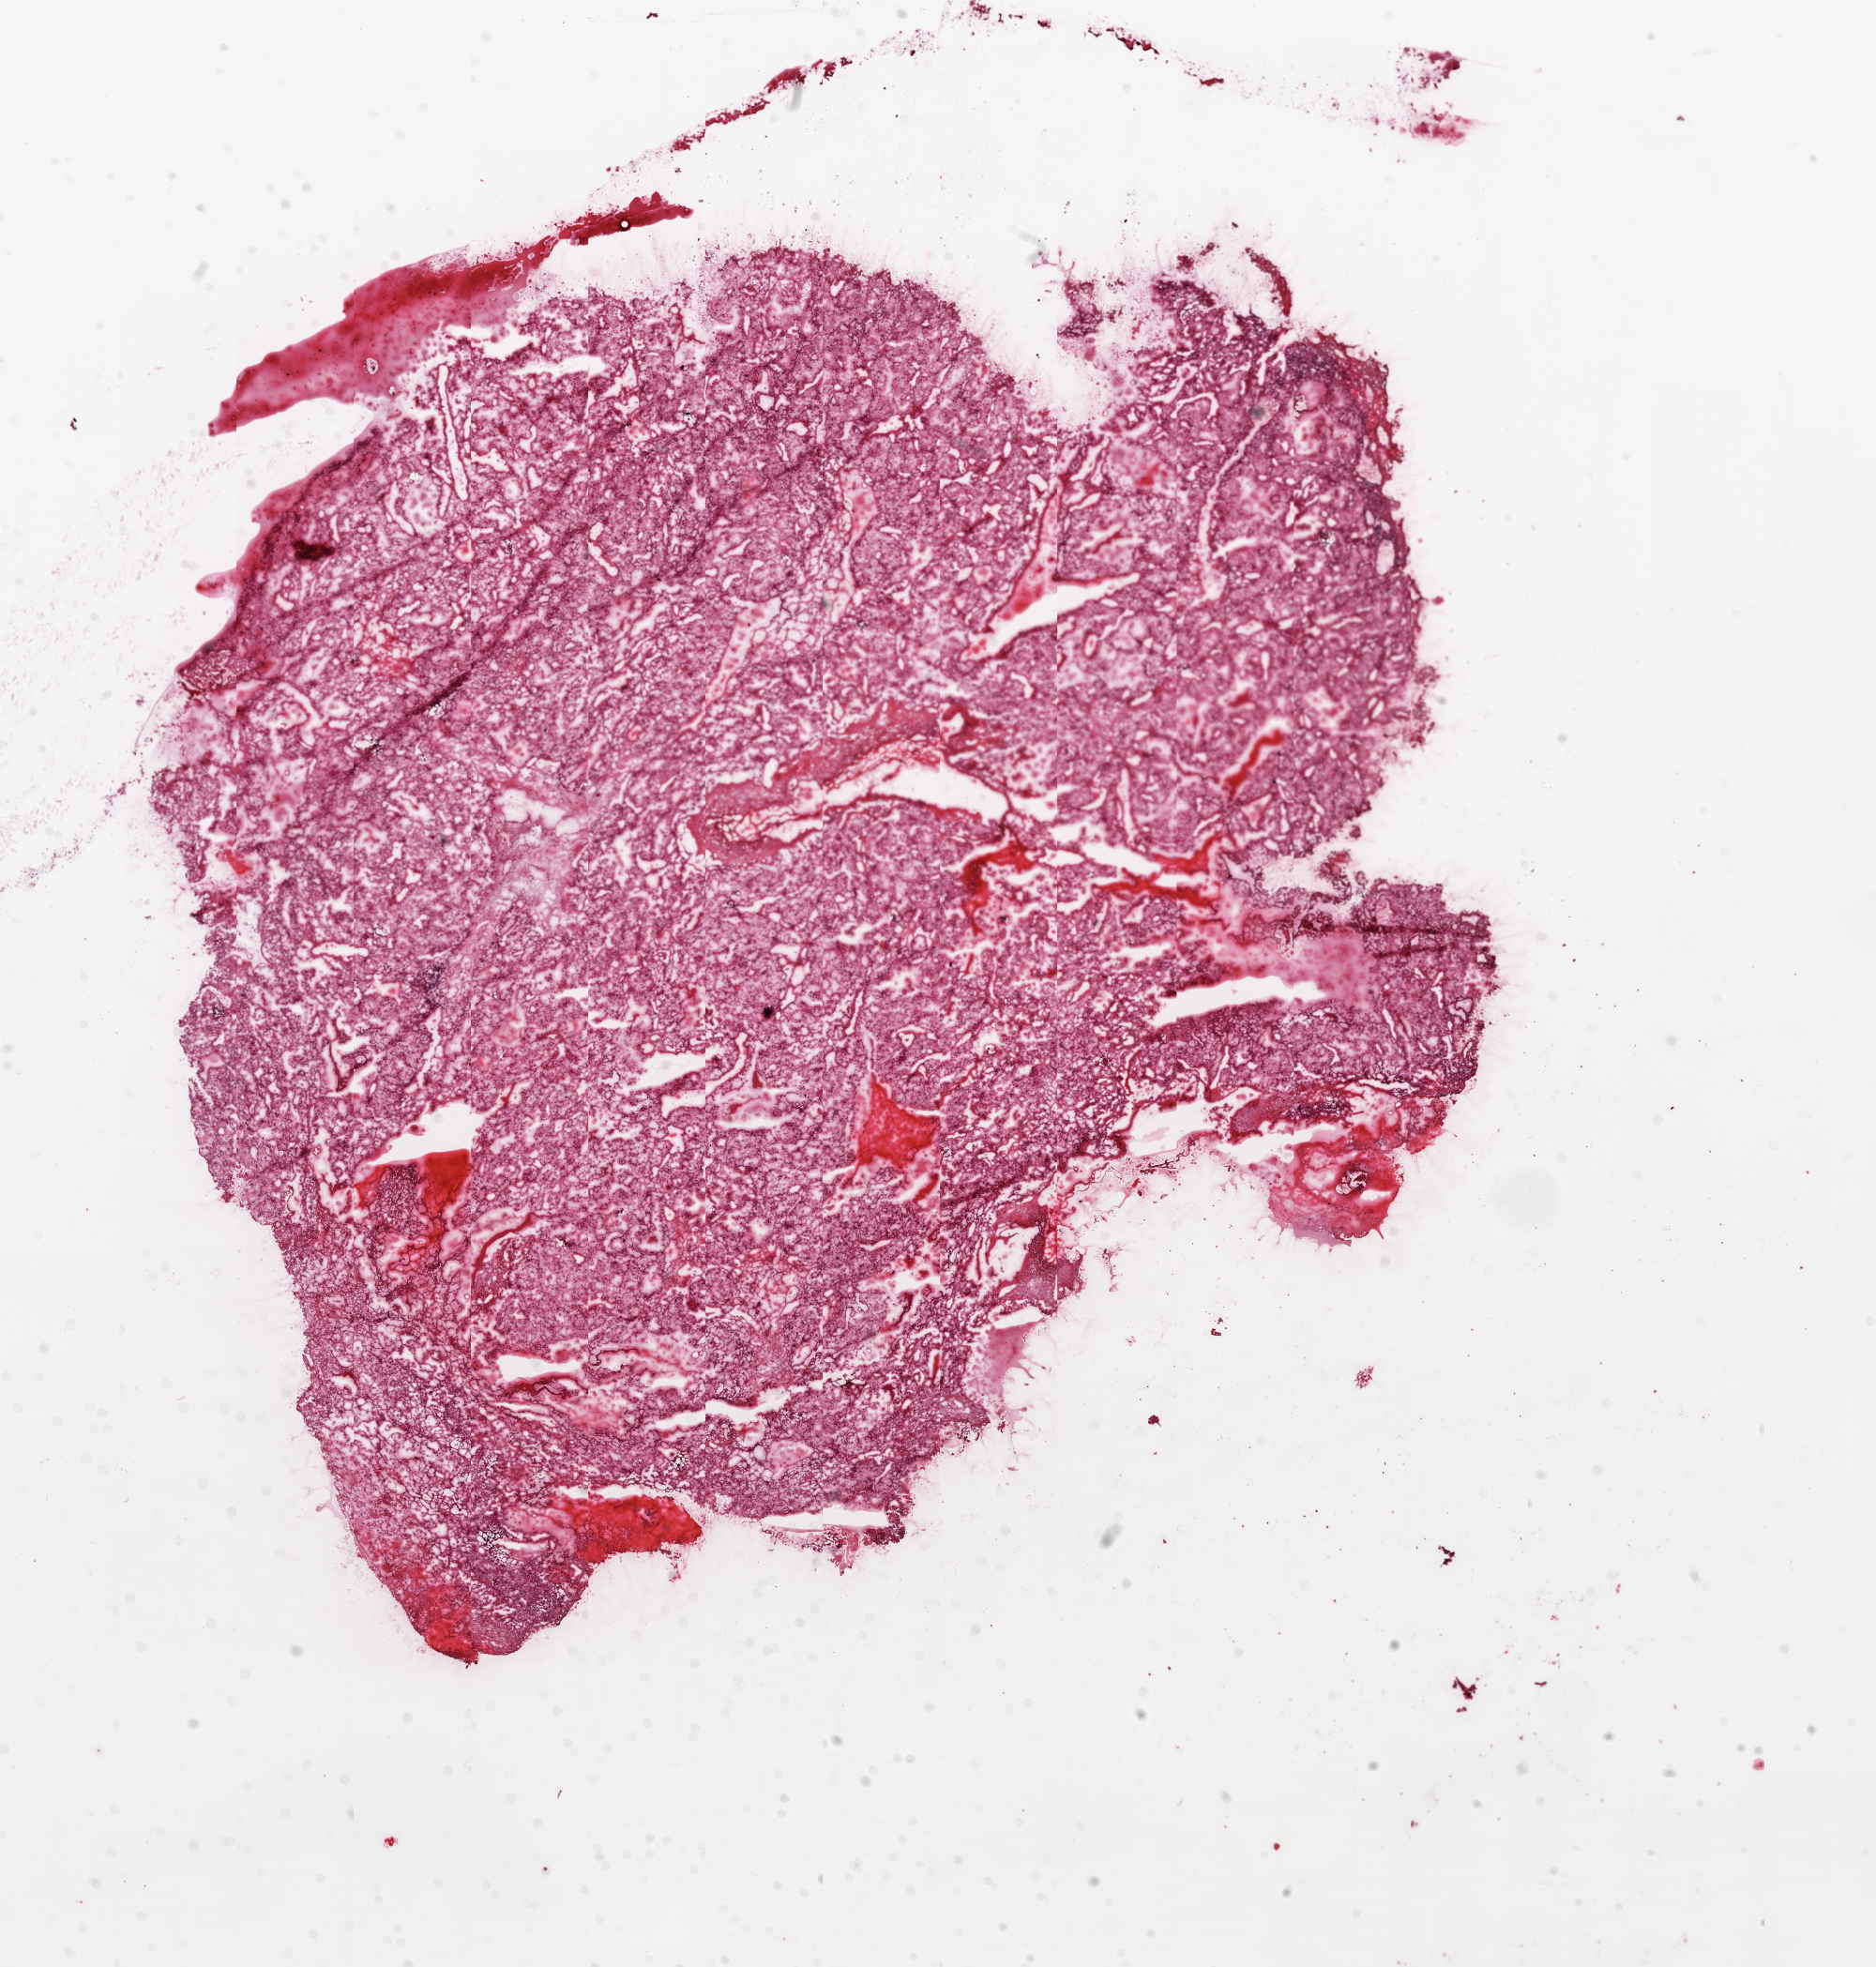
Whole-slide histology image, Hematoxylin and eosin (H&E) stained, whole scanned area (about 16.0 x 16.8 mm, slide scanned at 20x) shown as a low-resolution overview; frozen section; kidney, primary tumour sample. Male patient; age at initial diagnosis 46 years. Histologic grade: G3 (poorly differentiated). Slide review estimates, as recorded: tumour cells 90%, tumour nuclei 80%, normal cells 0%, stromal cells 10%, necrosis 0%.
TNM: T2 N0 M0. Pathologic diagnosis: Clear cell adenocarcinoma, NOS. AJCC pathologic stage: II. Lymph nodes positive (case pathology): 0 of 9 examined.